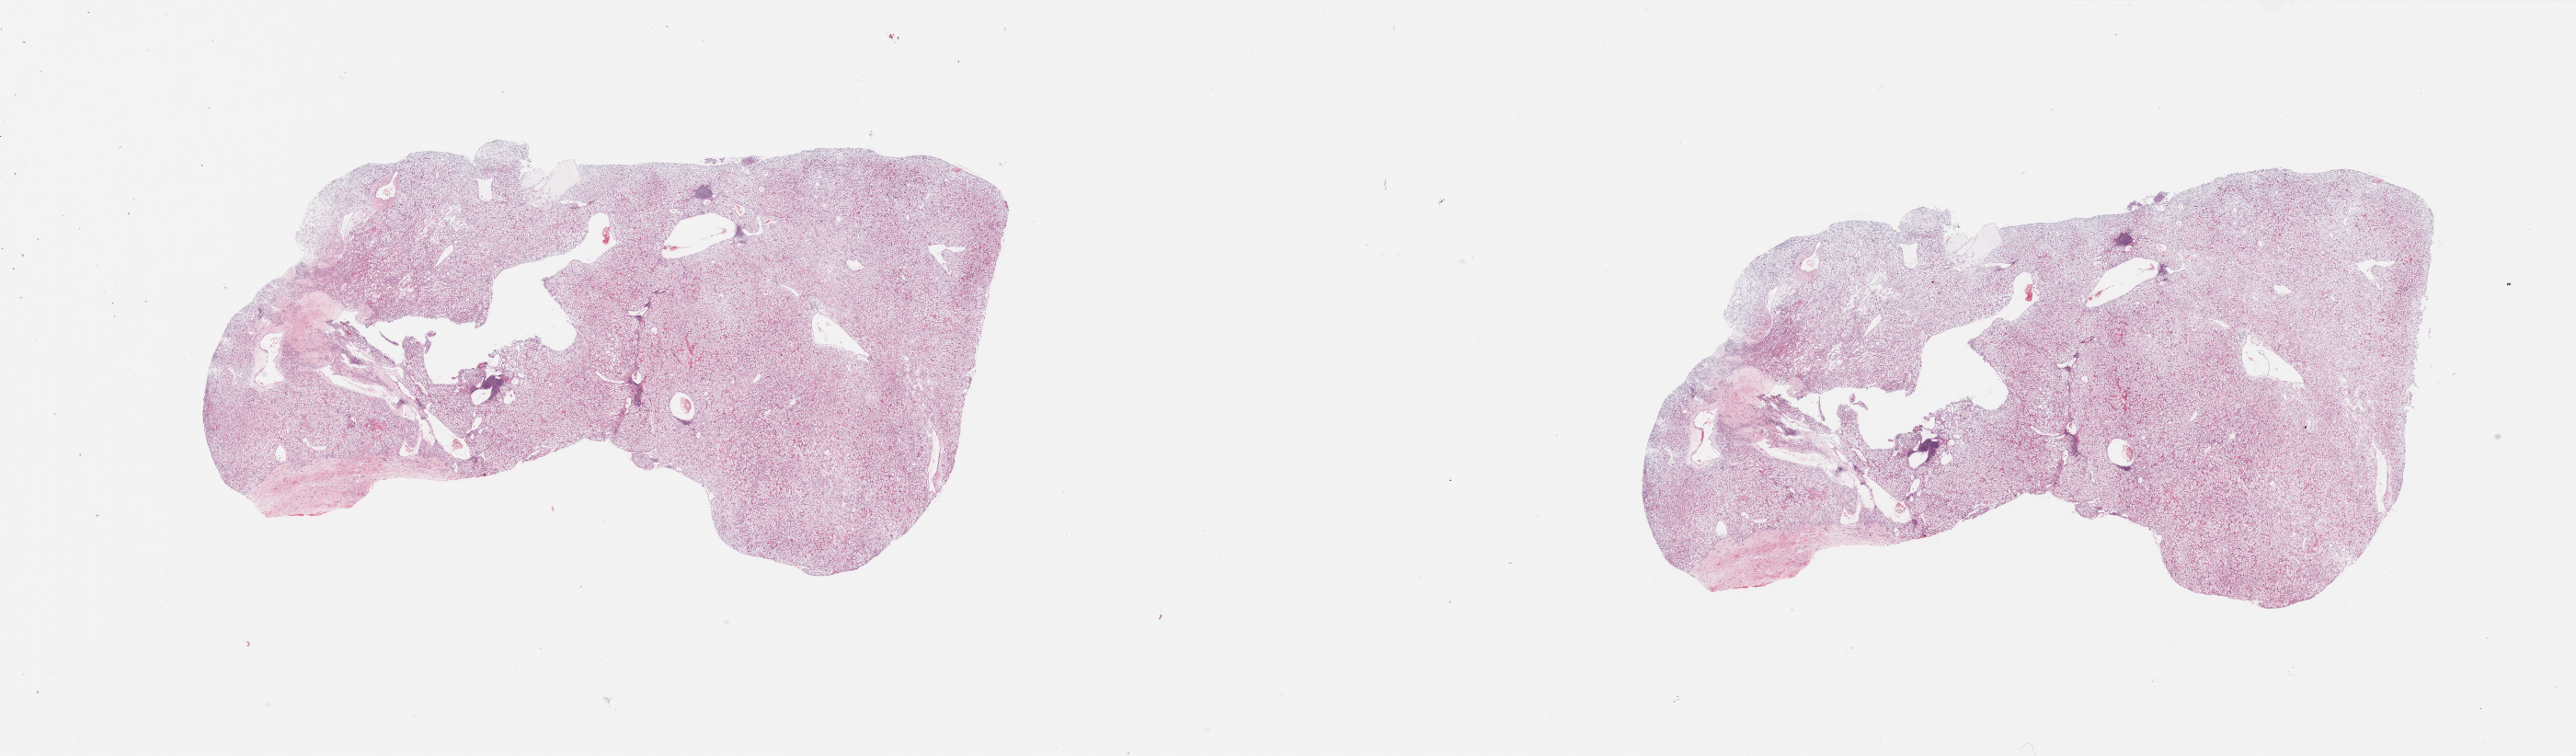
Digitized H&E tissue section (whole slide) — low-resolution overview of the scanned area, about 44.3 x 13.0 mm, tumour tissue sample, sampled site: kidney. Female, 72 y/o. Histologic grade: G4 (undifferentiated). Slide review estimates, as recorded: tumour nuclei 90%, necrosis 2%.
AJCC pathologic stage: III. Primary tumour site (as recorded): middle. Diagnosis: Renal cell carcinoma, NOS.